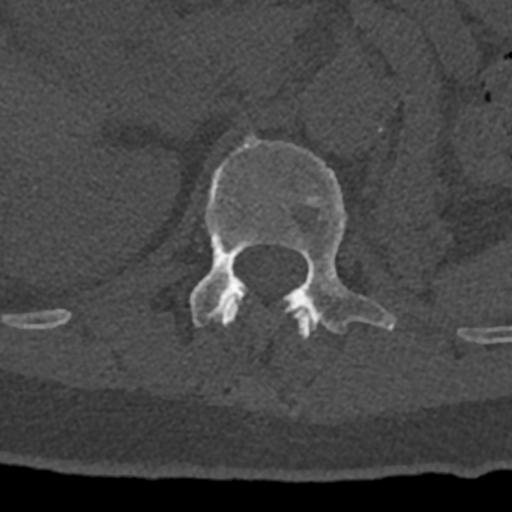
CT including the spine, one axial slice; slice 450 of 797 in the series (ordered by position); 120 kVp; bone window (W 1800 / L 400 HU); 0.5 mm slice thickness; 512 × 512 image matrix, field of view 160 × 160 mm. Male patient, age 74 years. Case-level facts recorded for this patient, not image findings: primary cancer: renal; vertebrae with lytic lesions (as recorded): T10, L1, L2, L3, L4, L5.
Annotated regions visible in this slice (semi-automatic segmentation, software-assisted and operator-edited):
- L1 vertebra: bounding box <190,135,396,333> (left, top, right, bottom; pixels)
- T12 vertebra: <220,298,315,340>